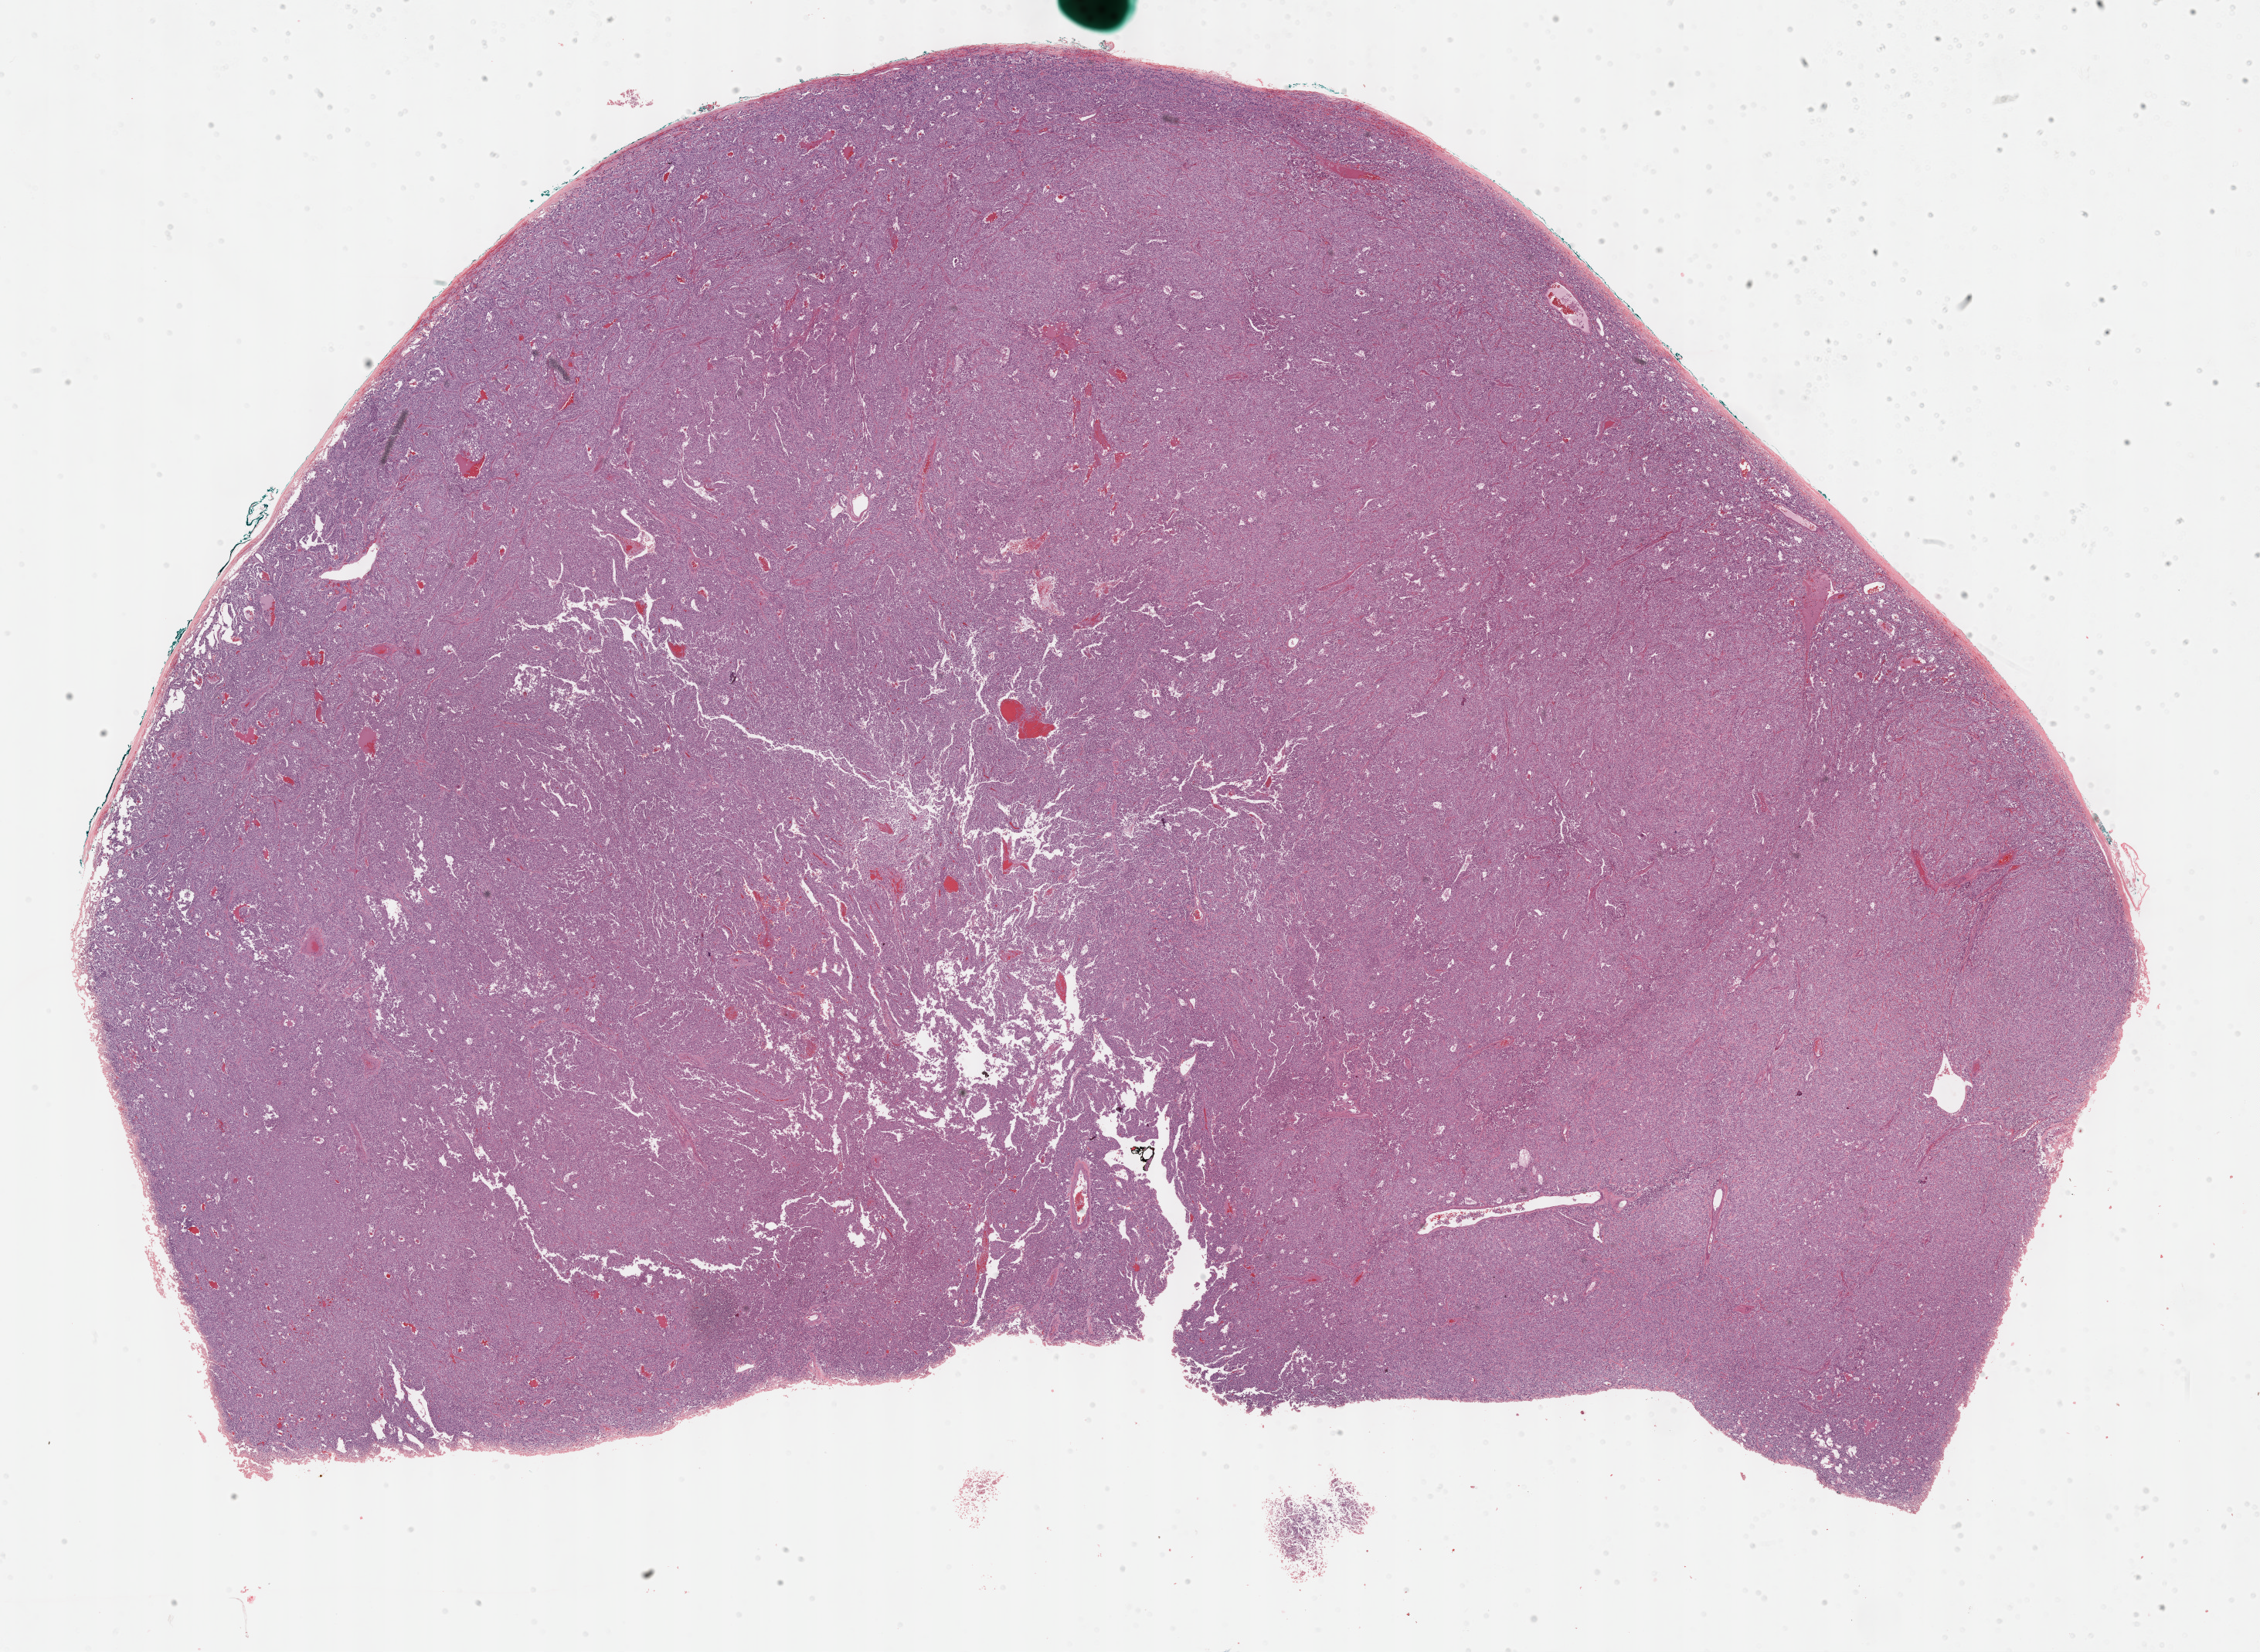
Whole-slide histology image, H&E-stained, a low-resolution overview of the entire scanned area, about 23.7 x 17.3 mm, FFPE section, adrenal gland, primary tumour sample. Patient: female, age at initial diagnosis 44 years.
Histologic diagnosis: Pheochromocytoma, NOS.